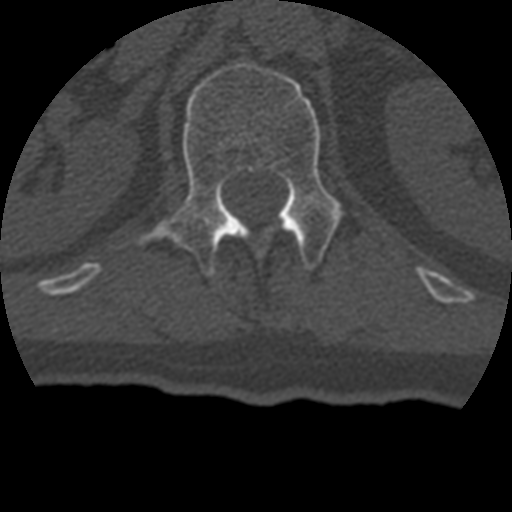
CT including the spine, one axial slice. Position 150 of 399 along the scan axis. Reconstruction kernel STANDARD. 120 kVp. Bone window (W 1800 / L 400 HU). 1.25 mm slice thickness. 512 × 512 image matrix, field of view 160 × 160 mm. Patient age 69 years. Case-level facts recorded for this patient, not image findings: primary cancer: prostate.
Structures marked on this image (semi-automatically segmented with operator editing):
- L1 vertebra: bounding box [x1, y1, x2, y2] px = [139, 62, 343, 278]